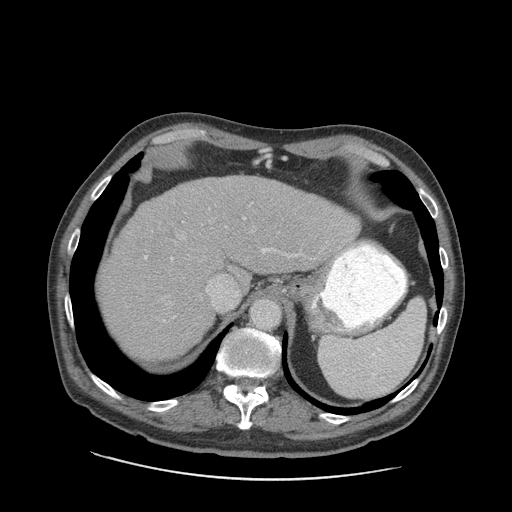
Contrast-enhanced abdominal CT (liver protocol), one axial slice. Slice 68 of 89 in the series (ordered by position). 140 kVp. Soft-tissue window (W 400 / L 40 HU). 2.5 mm slice thickness. 512 × 512 image matrix, field of view 420 × 420 mm. From the clinical record (not read from this slice): diagnosis: hepatocellular carcinoma (patient treated with transarterial chemoembolisation; whether this scan precedes or follows treatment is not stated here); TNM stage (as recorded): Stage-I; Child-Pugh class: A.
Outlined on this slice (semi-automatically segmented with operator editing):
- liver parenchyma outside the tumour (the mass and vessels are separate outlines, so this box may not span the whole liver): bounding box [x1, y1, x2, y2] px = [100, 174, 357, 360]
- liver vessels: [145, 202, 341, 322]